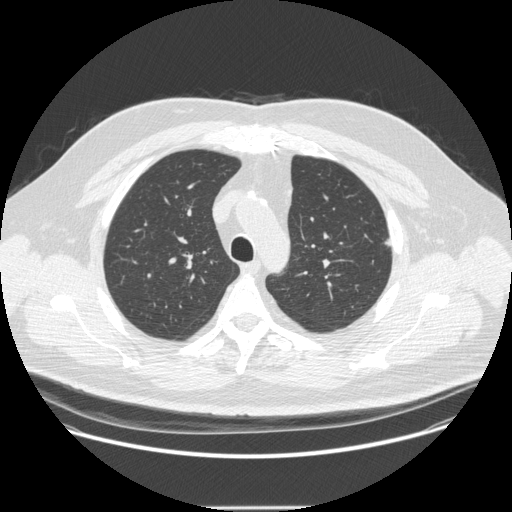
Low-dose screening chest CT, axial slice; second annual screen; lung window (W 1500 / L -600 HU); standard (soft-tissue) reconstruction kernel (STANDARD). Male participant, aged 55 years at enrolment.
- Expert reader's lesion annotation, bounding box [x1, y1, x2, y2] px = [373, 232, 405, 252].
- The screening reader recorded 2 non-calcified nodules or masses ≥4 mm on this exam (left upper lobe, left upper lobe); which of them this box marks is not recorded.